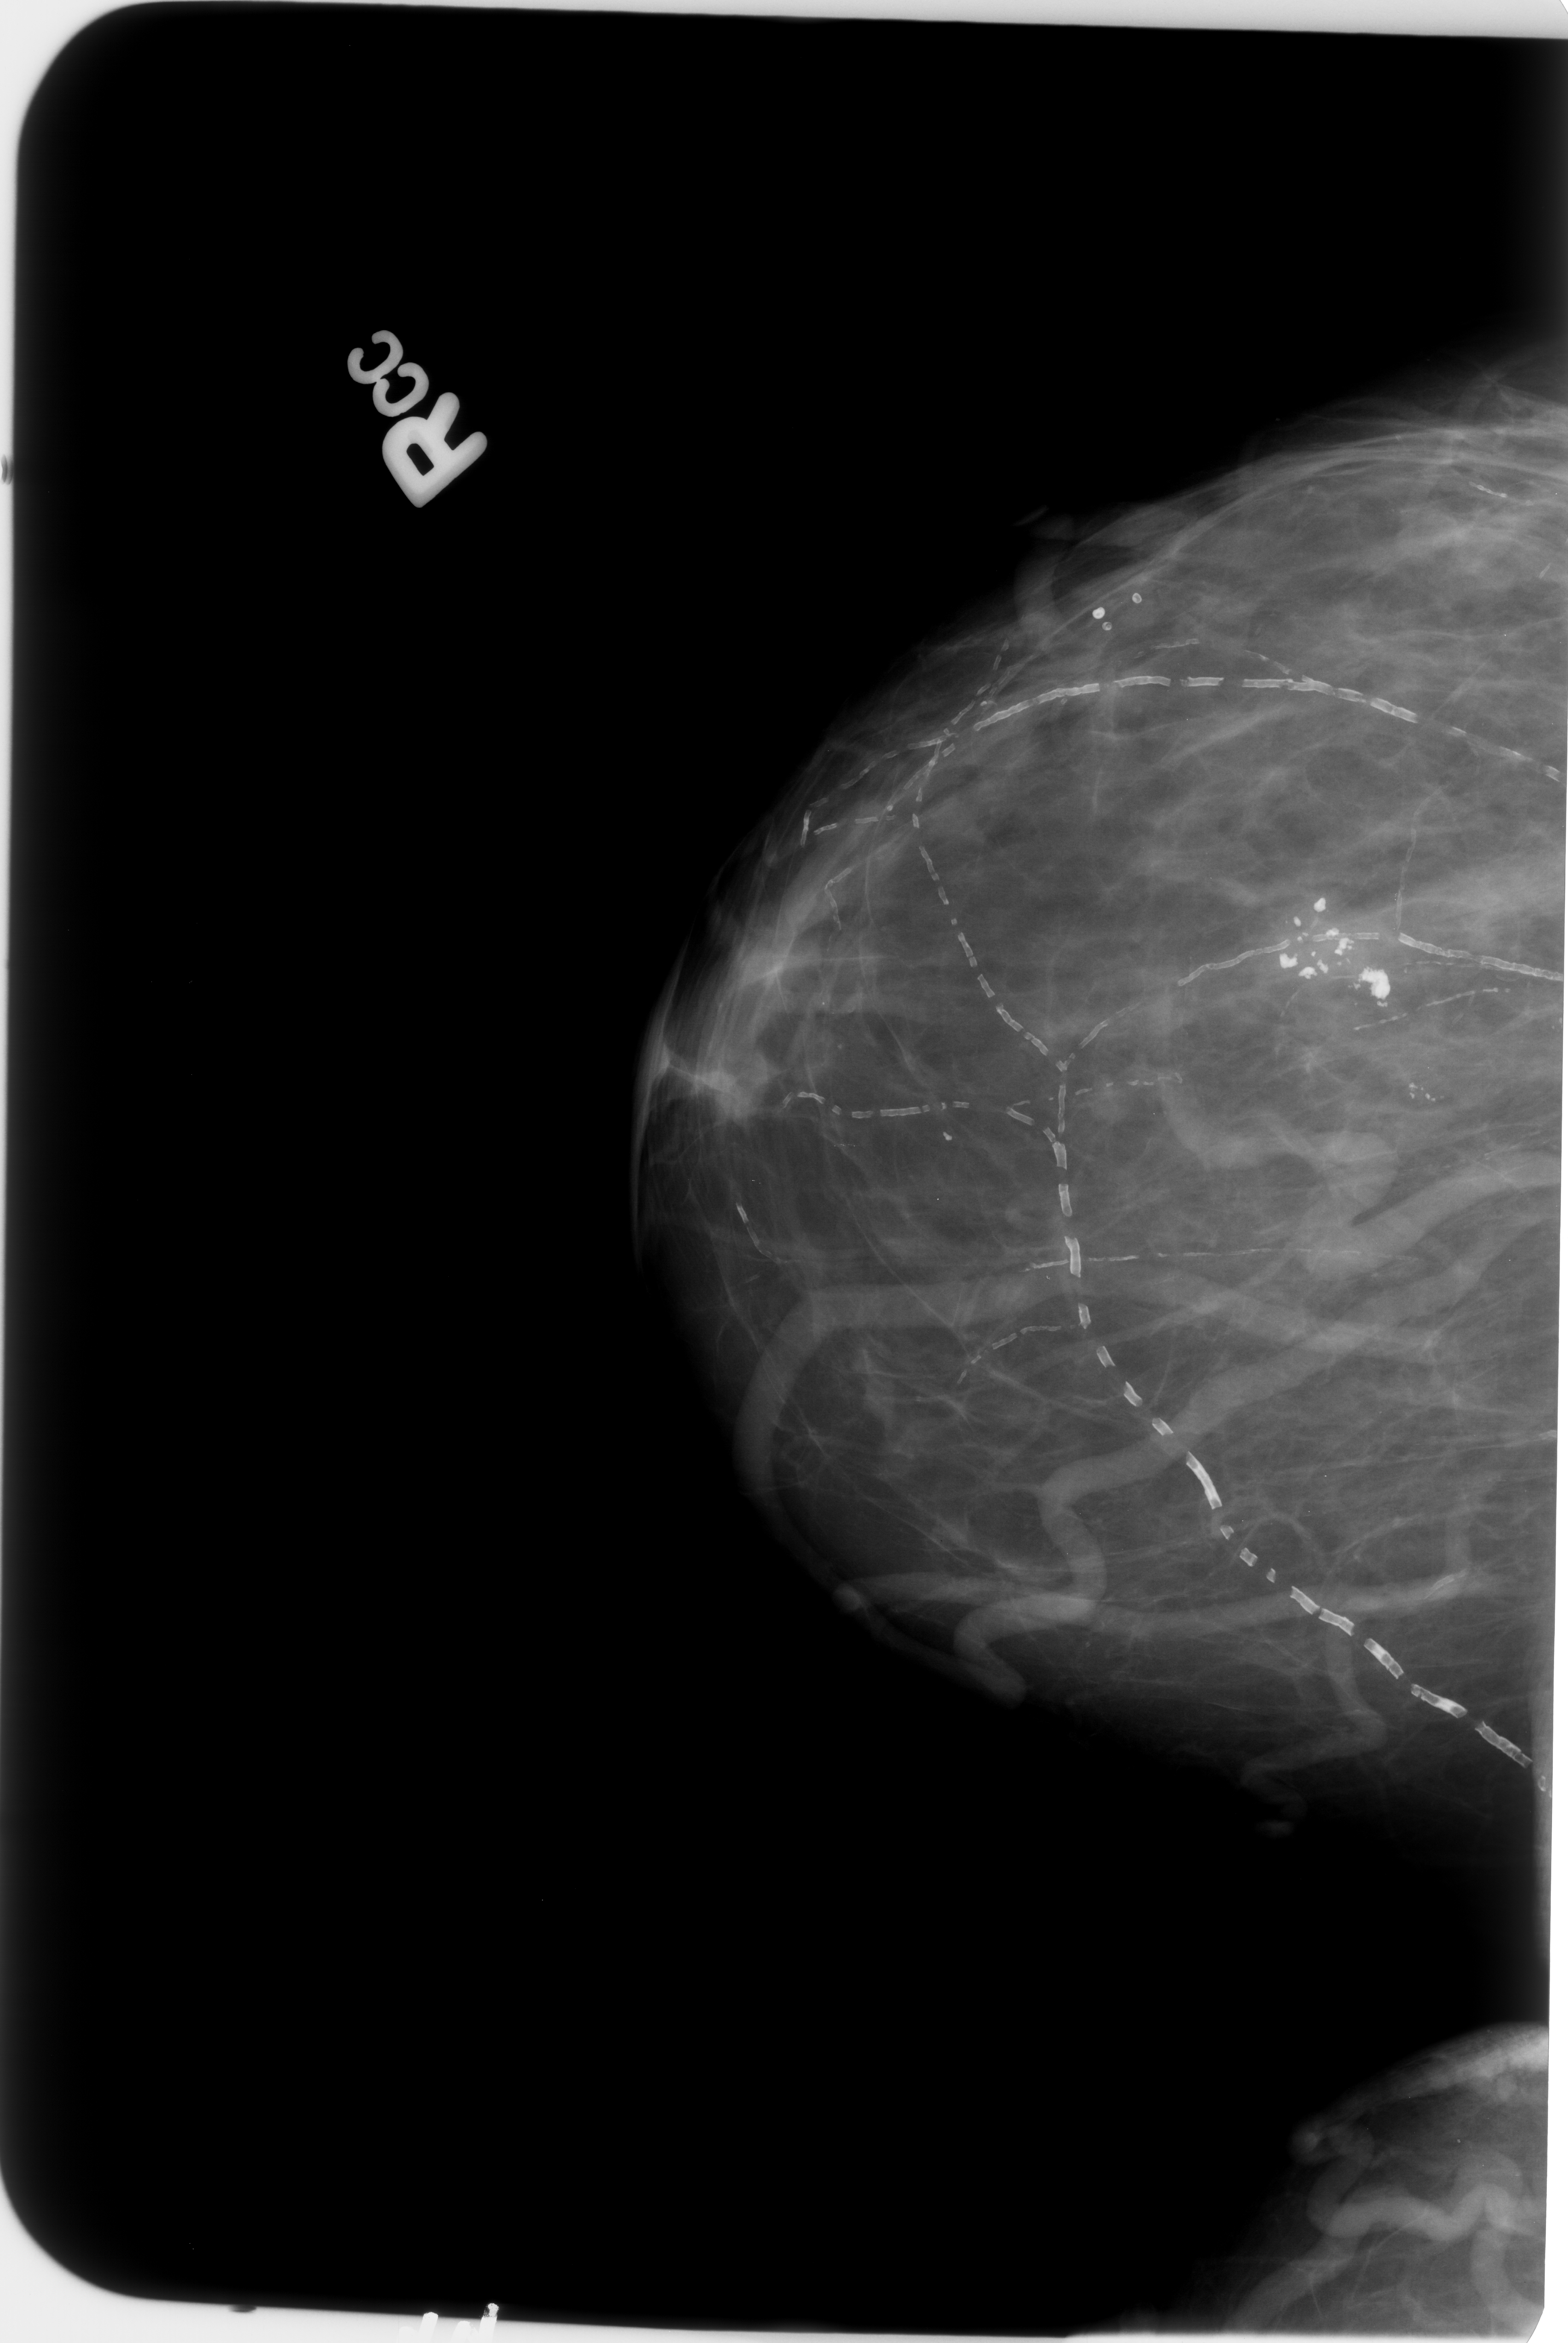
Digitized screen-film mammogram; right breast; craniocaudal (CC) view; breast composition: almost entirely fatty (BI-RADS density category 1 of 4).
Calcifications, morphology coarse / pleomorphic, distribution clustered; BI-RADS assessment category 2; subtlety rating 5 on a 1 (subtle) to 5 (obvious) scale; pathology (as recorded): benign.